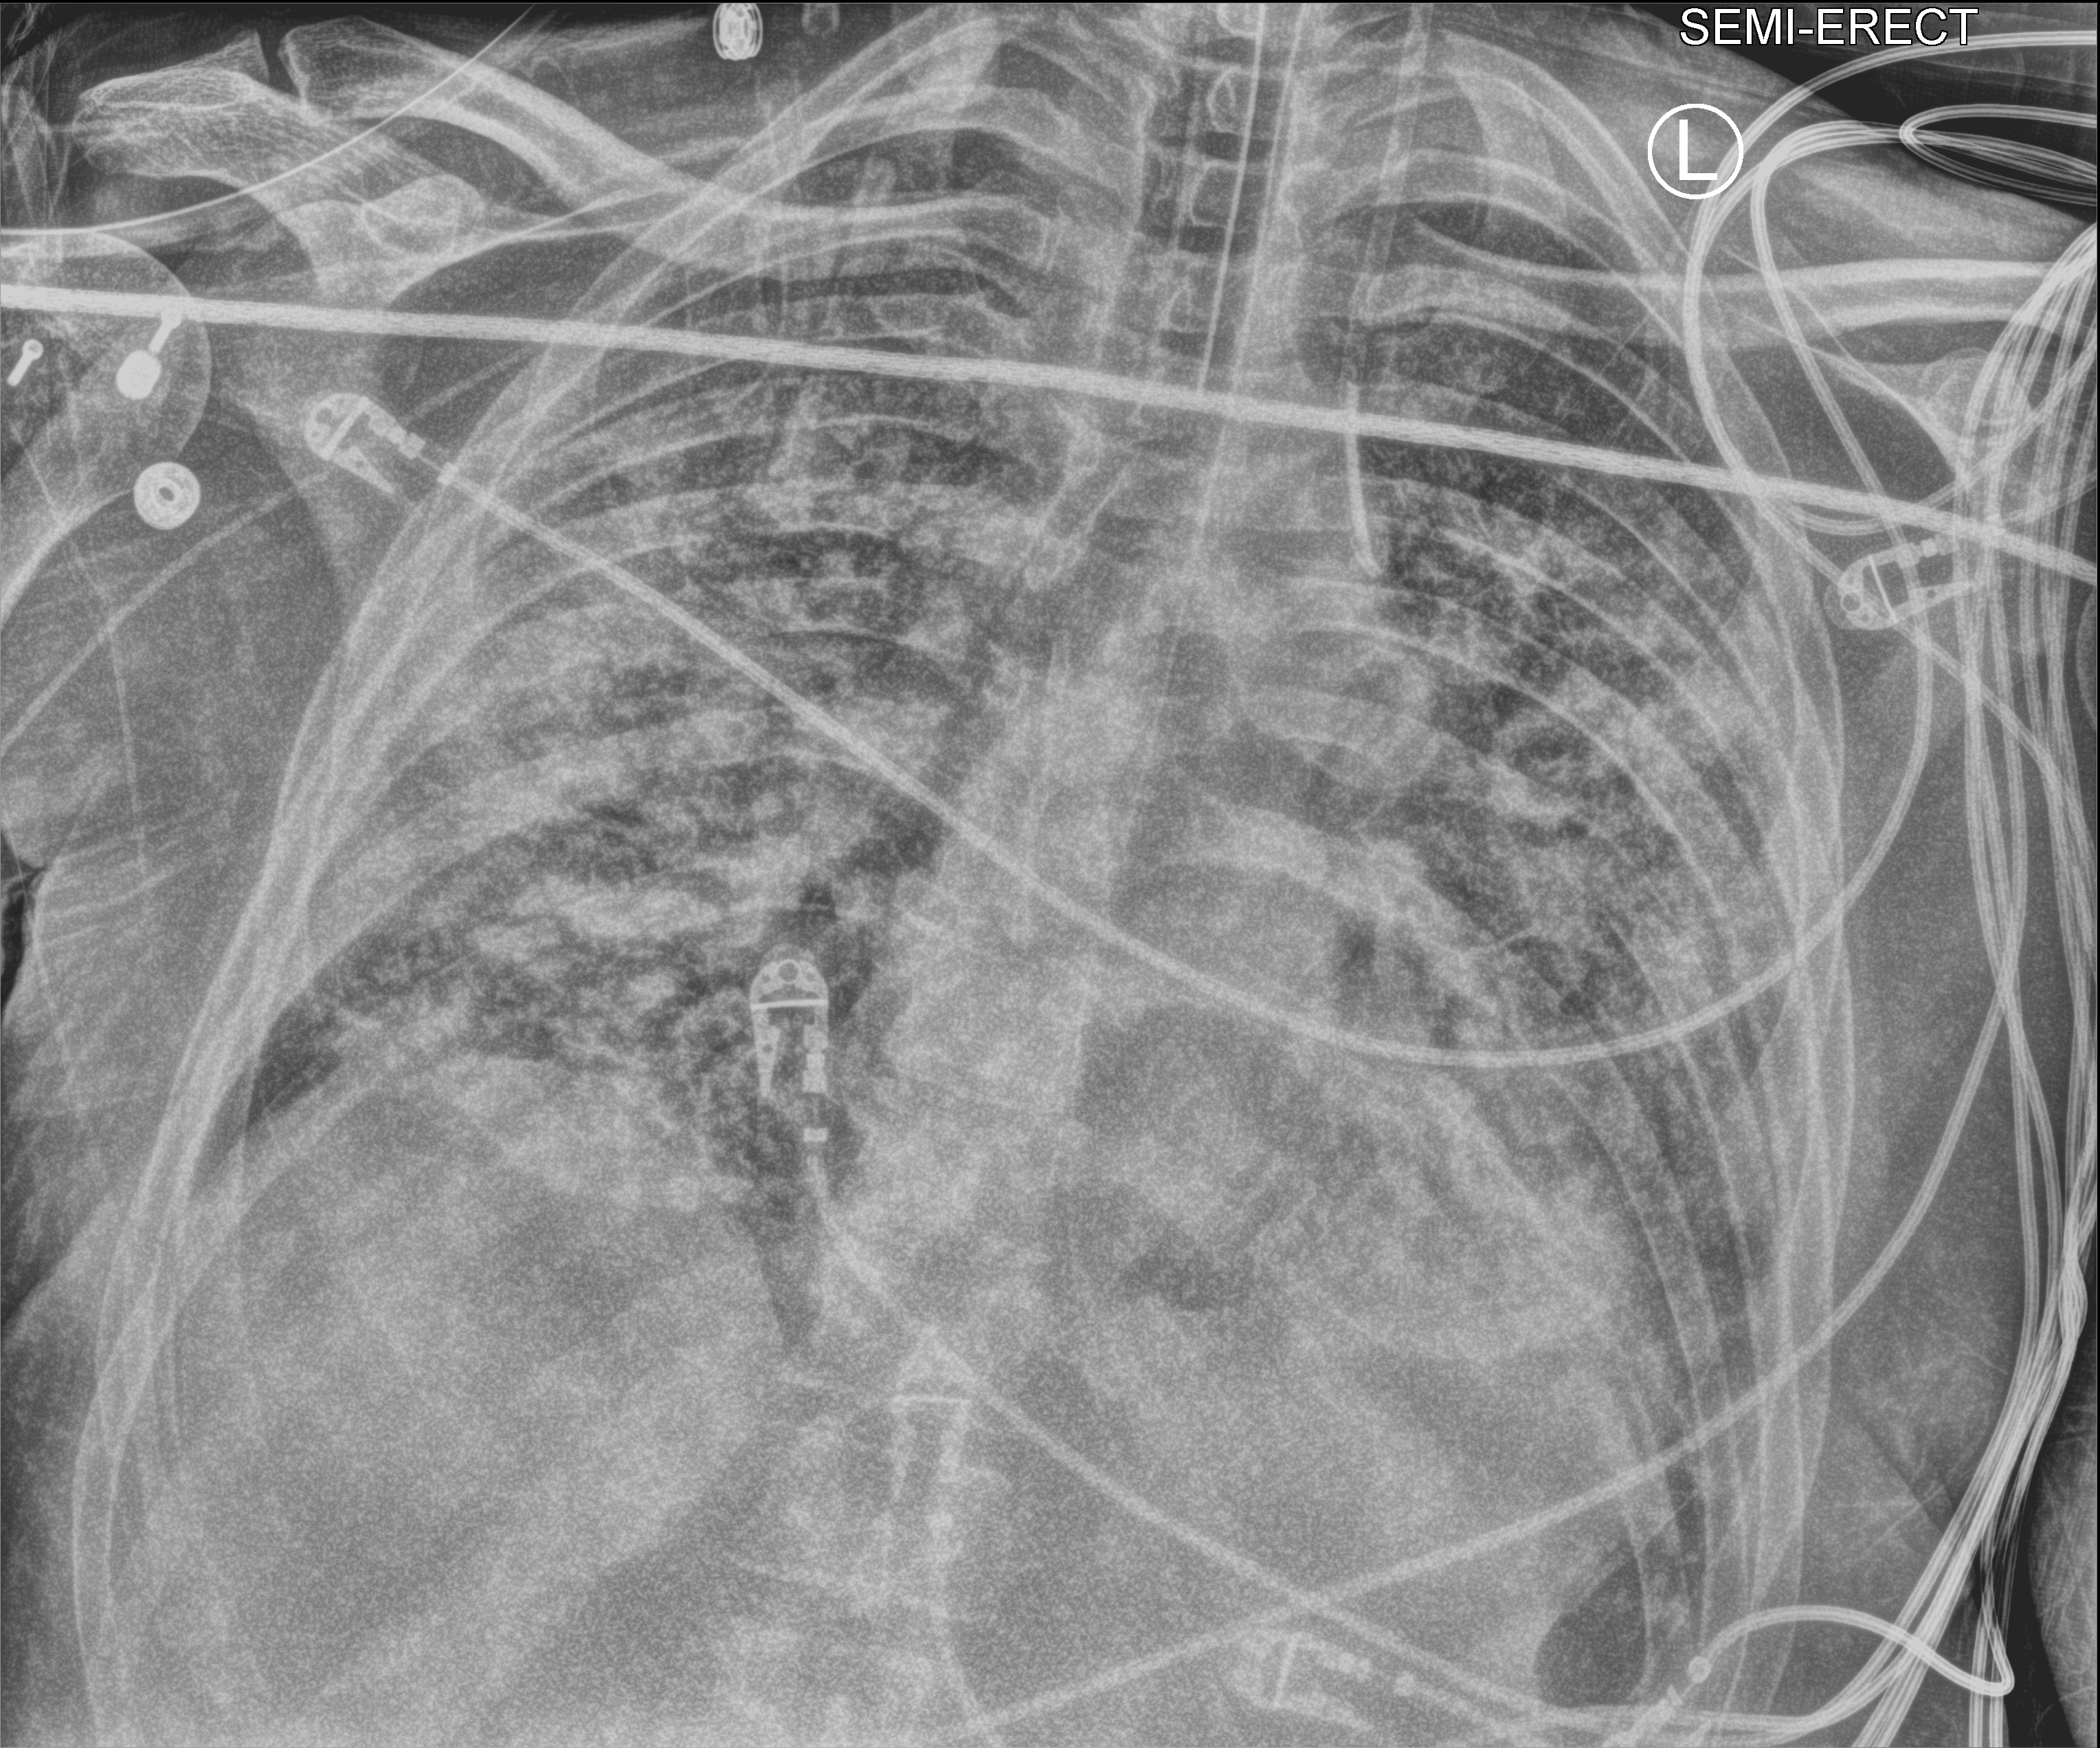
Portable chest radiograph, anteroposterior (AP) projection. Patient hospitalised with COVID-19; male, aged 18–59 years.
Admission-level facts for this patient (not findings on this image; timing relative to this image not recorded):
- mechanically ventilated during this hospital stay: yes